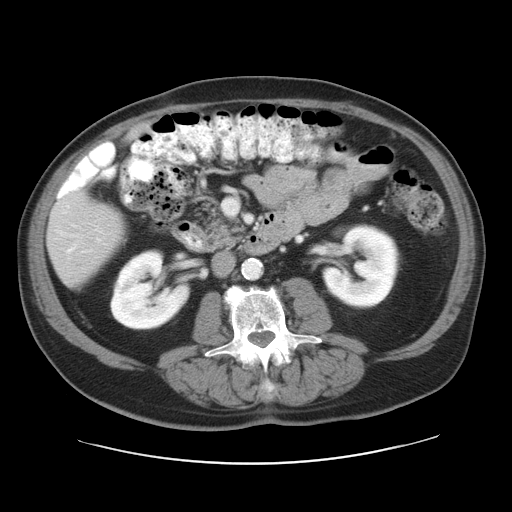
Contrast-enhanced abdominal CT, one axial slice; position 10 of 28 along the scan axis; intravenous contrast given; soft-tissue window (W 400 / L 40 HU); 512 × 512 image matrix, field of view 402 × 402 mm. Male patient, age 74 years. Case-level facts recorded for this patient, not image findings: diagnosis: colorectal cancer liver metastases, imaged before liver resection; multiple liver metastases: no; largest metastasis: 5 cm; disease in both lobes: no.
Annotated regions visible in this slice (expert manual segmentation):
- hepatic veins: bounding box <97,238,100,241> (left, top, right, bottom; pixels)
- liver: <48,197,122,284>
- planned liver remnant (the part of the liver to remain after resection): <48,197,122,284>